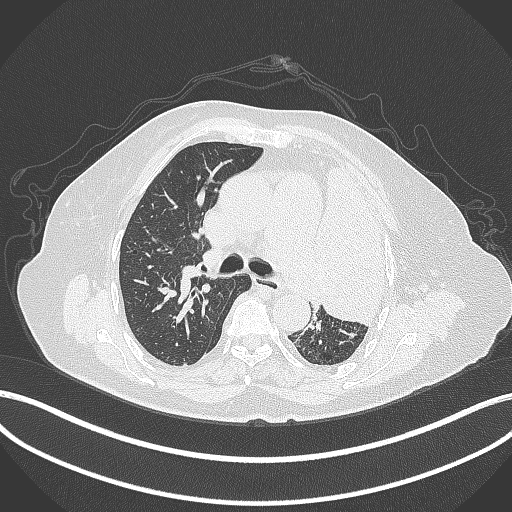
Chest CT, one axial slice; slice 249 of 399 in the series (ordered by position); reconstruction kernel B70f; lung window (W 1500 / L -600 HU); 1 mm slice thickness; 512 × 512 image matrix, field of view 400 × 400 mm. Patient: female, 75 years. Case-level facts recorded for this patient, not image findings: clinical TNM (as recorded): T3 N3 M1.
Annotated regions visible in this slice (rectangle marked by the reading radiologist):
- lung tumour (recorded histology: adenocarcinoma): bounding box <316,154,392,326> (left, top, right, bottom; pixels)